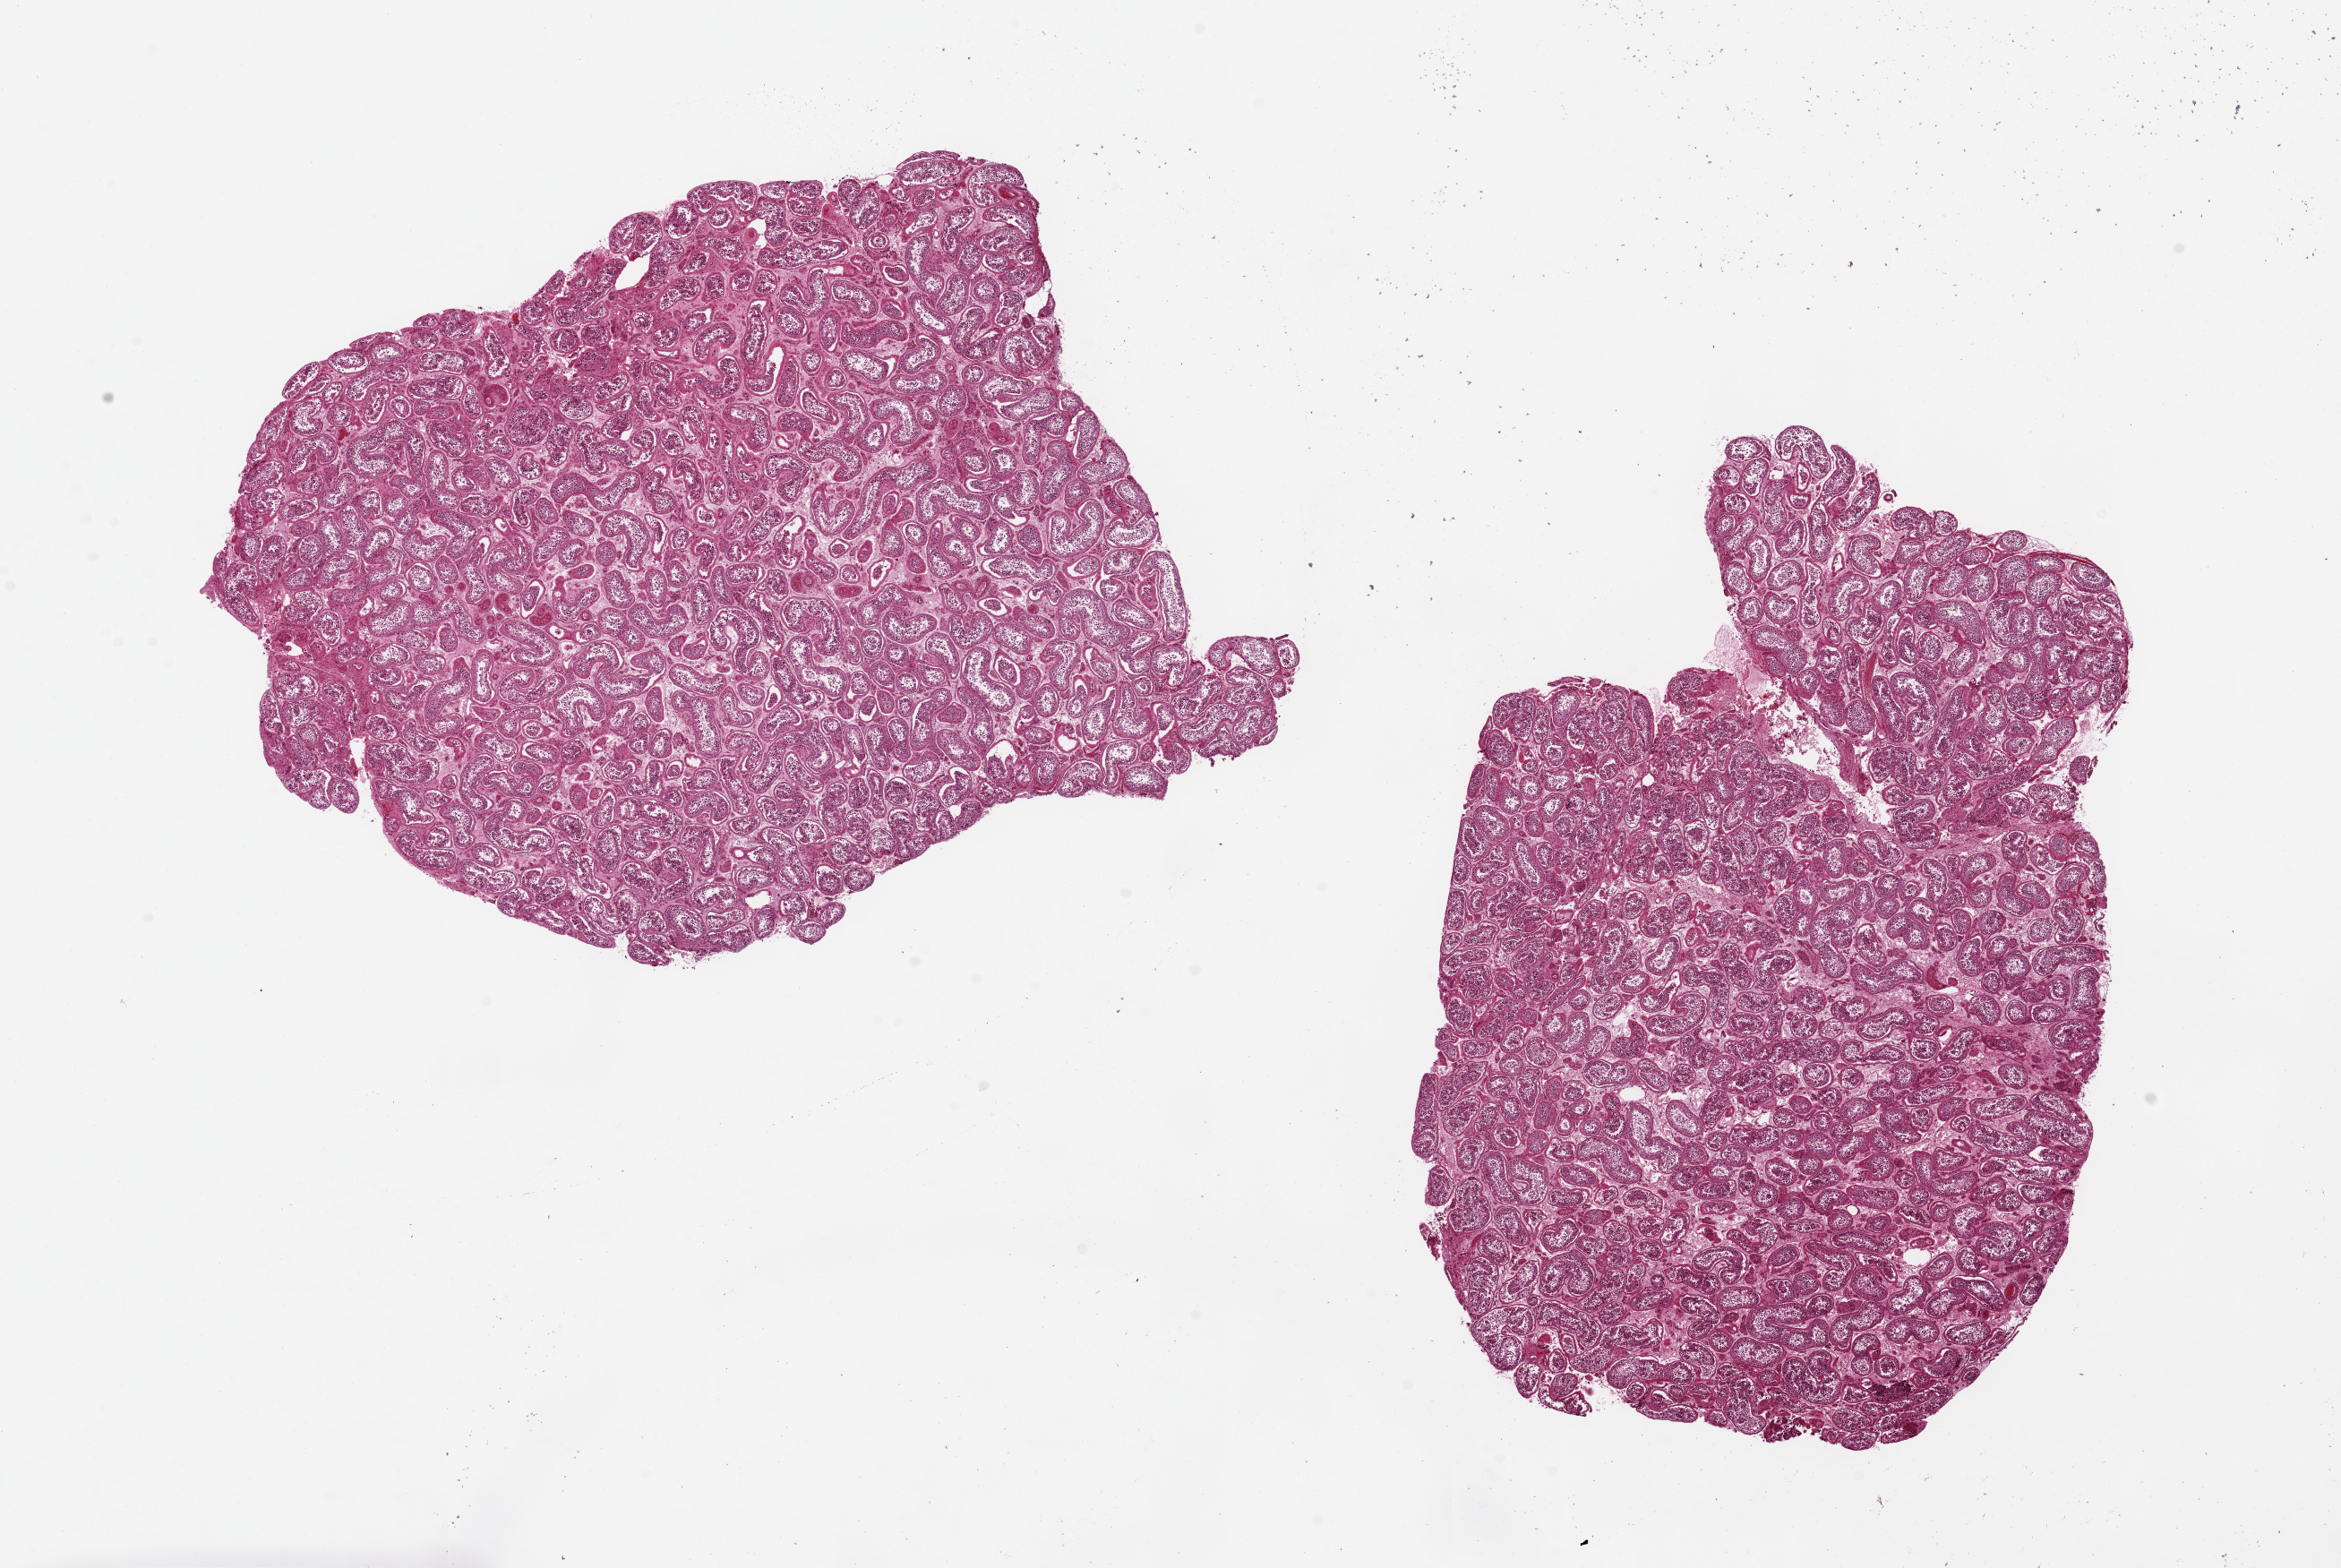
Digitized H&E-stained section, a low-resolution overview of the entire scanned area, about 20.7 x 13.8 mm; PAXgene-fixed paraffin-embedded (PFPE) section; sampled site (target tissue): testis; tissue donor sample. Male donor.
Reviewer comment on this tissue sample: 2 pieces, 8x6mm. Spermatogenesis is present but badly autolyzed.